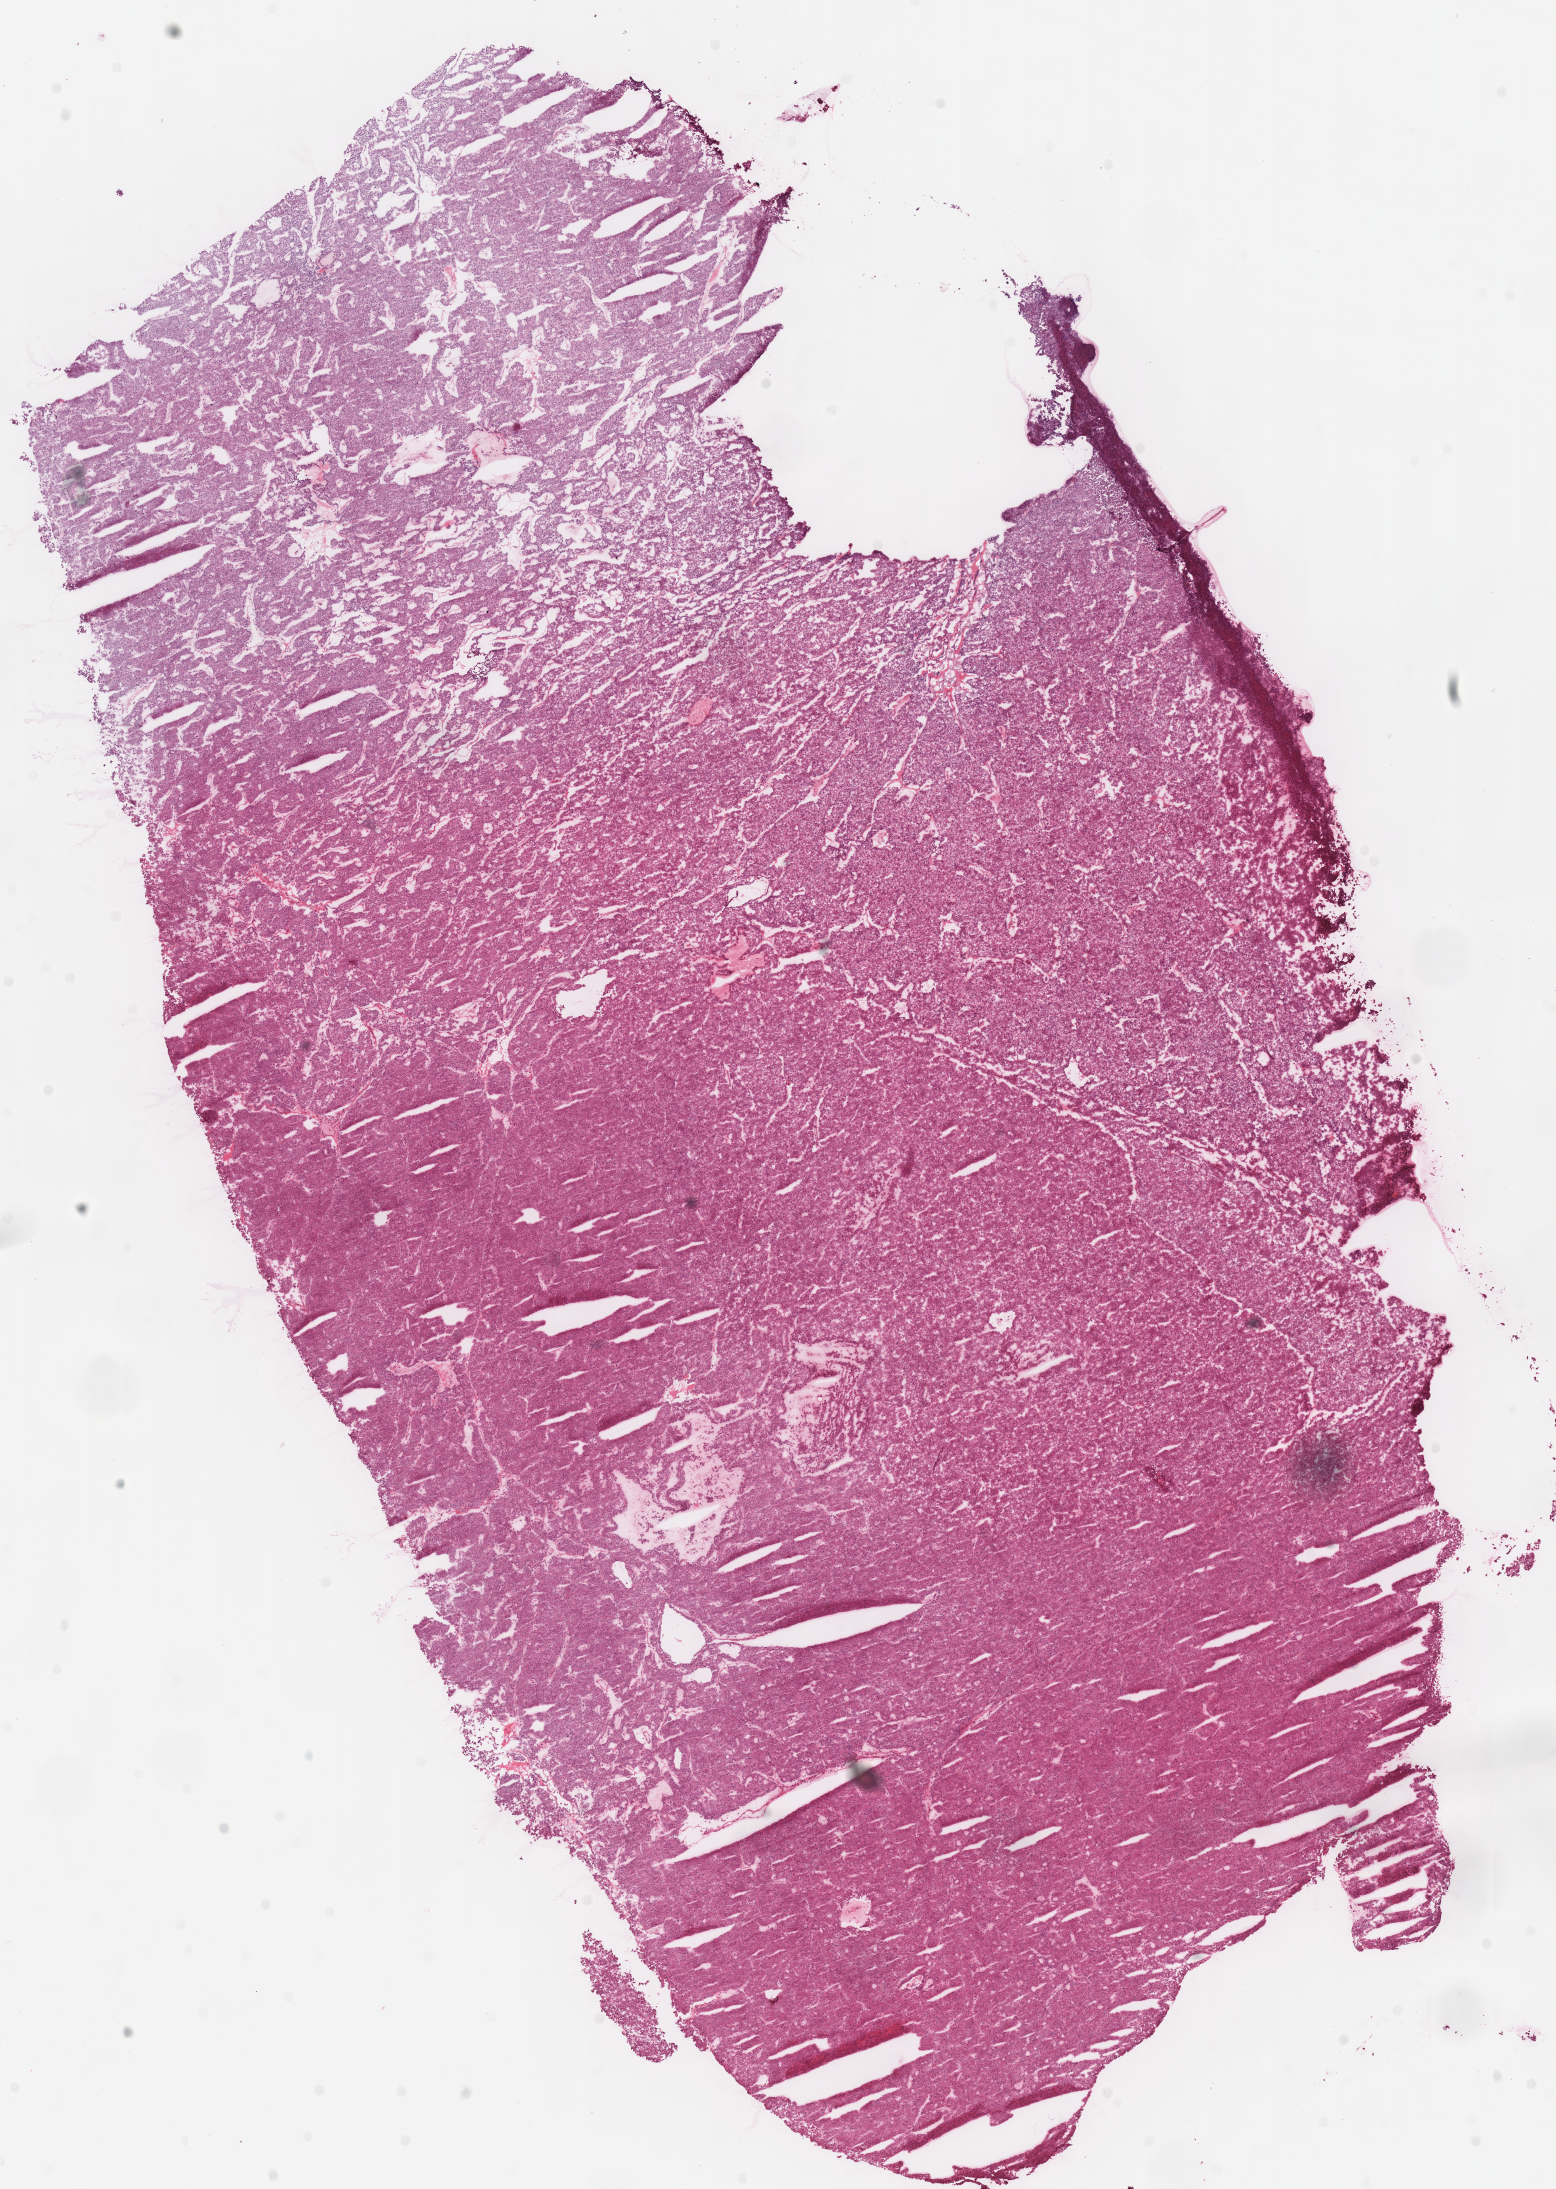
H&E-stained whole-slide image — low-resolution overview of the scanned area, about 12.2 x 17.2 mm (slide scanned at 40x), frozen section from the top of the tissue portion, primary tumour sample from the kidney. Patient: female, age at initial diagnosis 44 years. Composition of this section per pathologist review: tumour cells 100%, tumour nuclei 95%, normal cells 0%, stromal cells 0%, necrosis 0%. Inflammatory infiltration, as recorded: lymphocyte infiltration 1%, monocyte infiltration 0%, neutrophil infiltration 0%.
• lymph nodes positive (case pathology): 0 of 8 examined
• histologic diagnosis: Renal cell carcinoma, chromophobe type
• AJCC pathologic stage: II